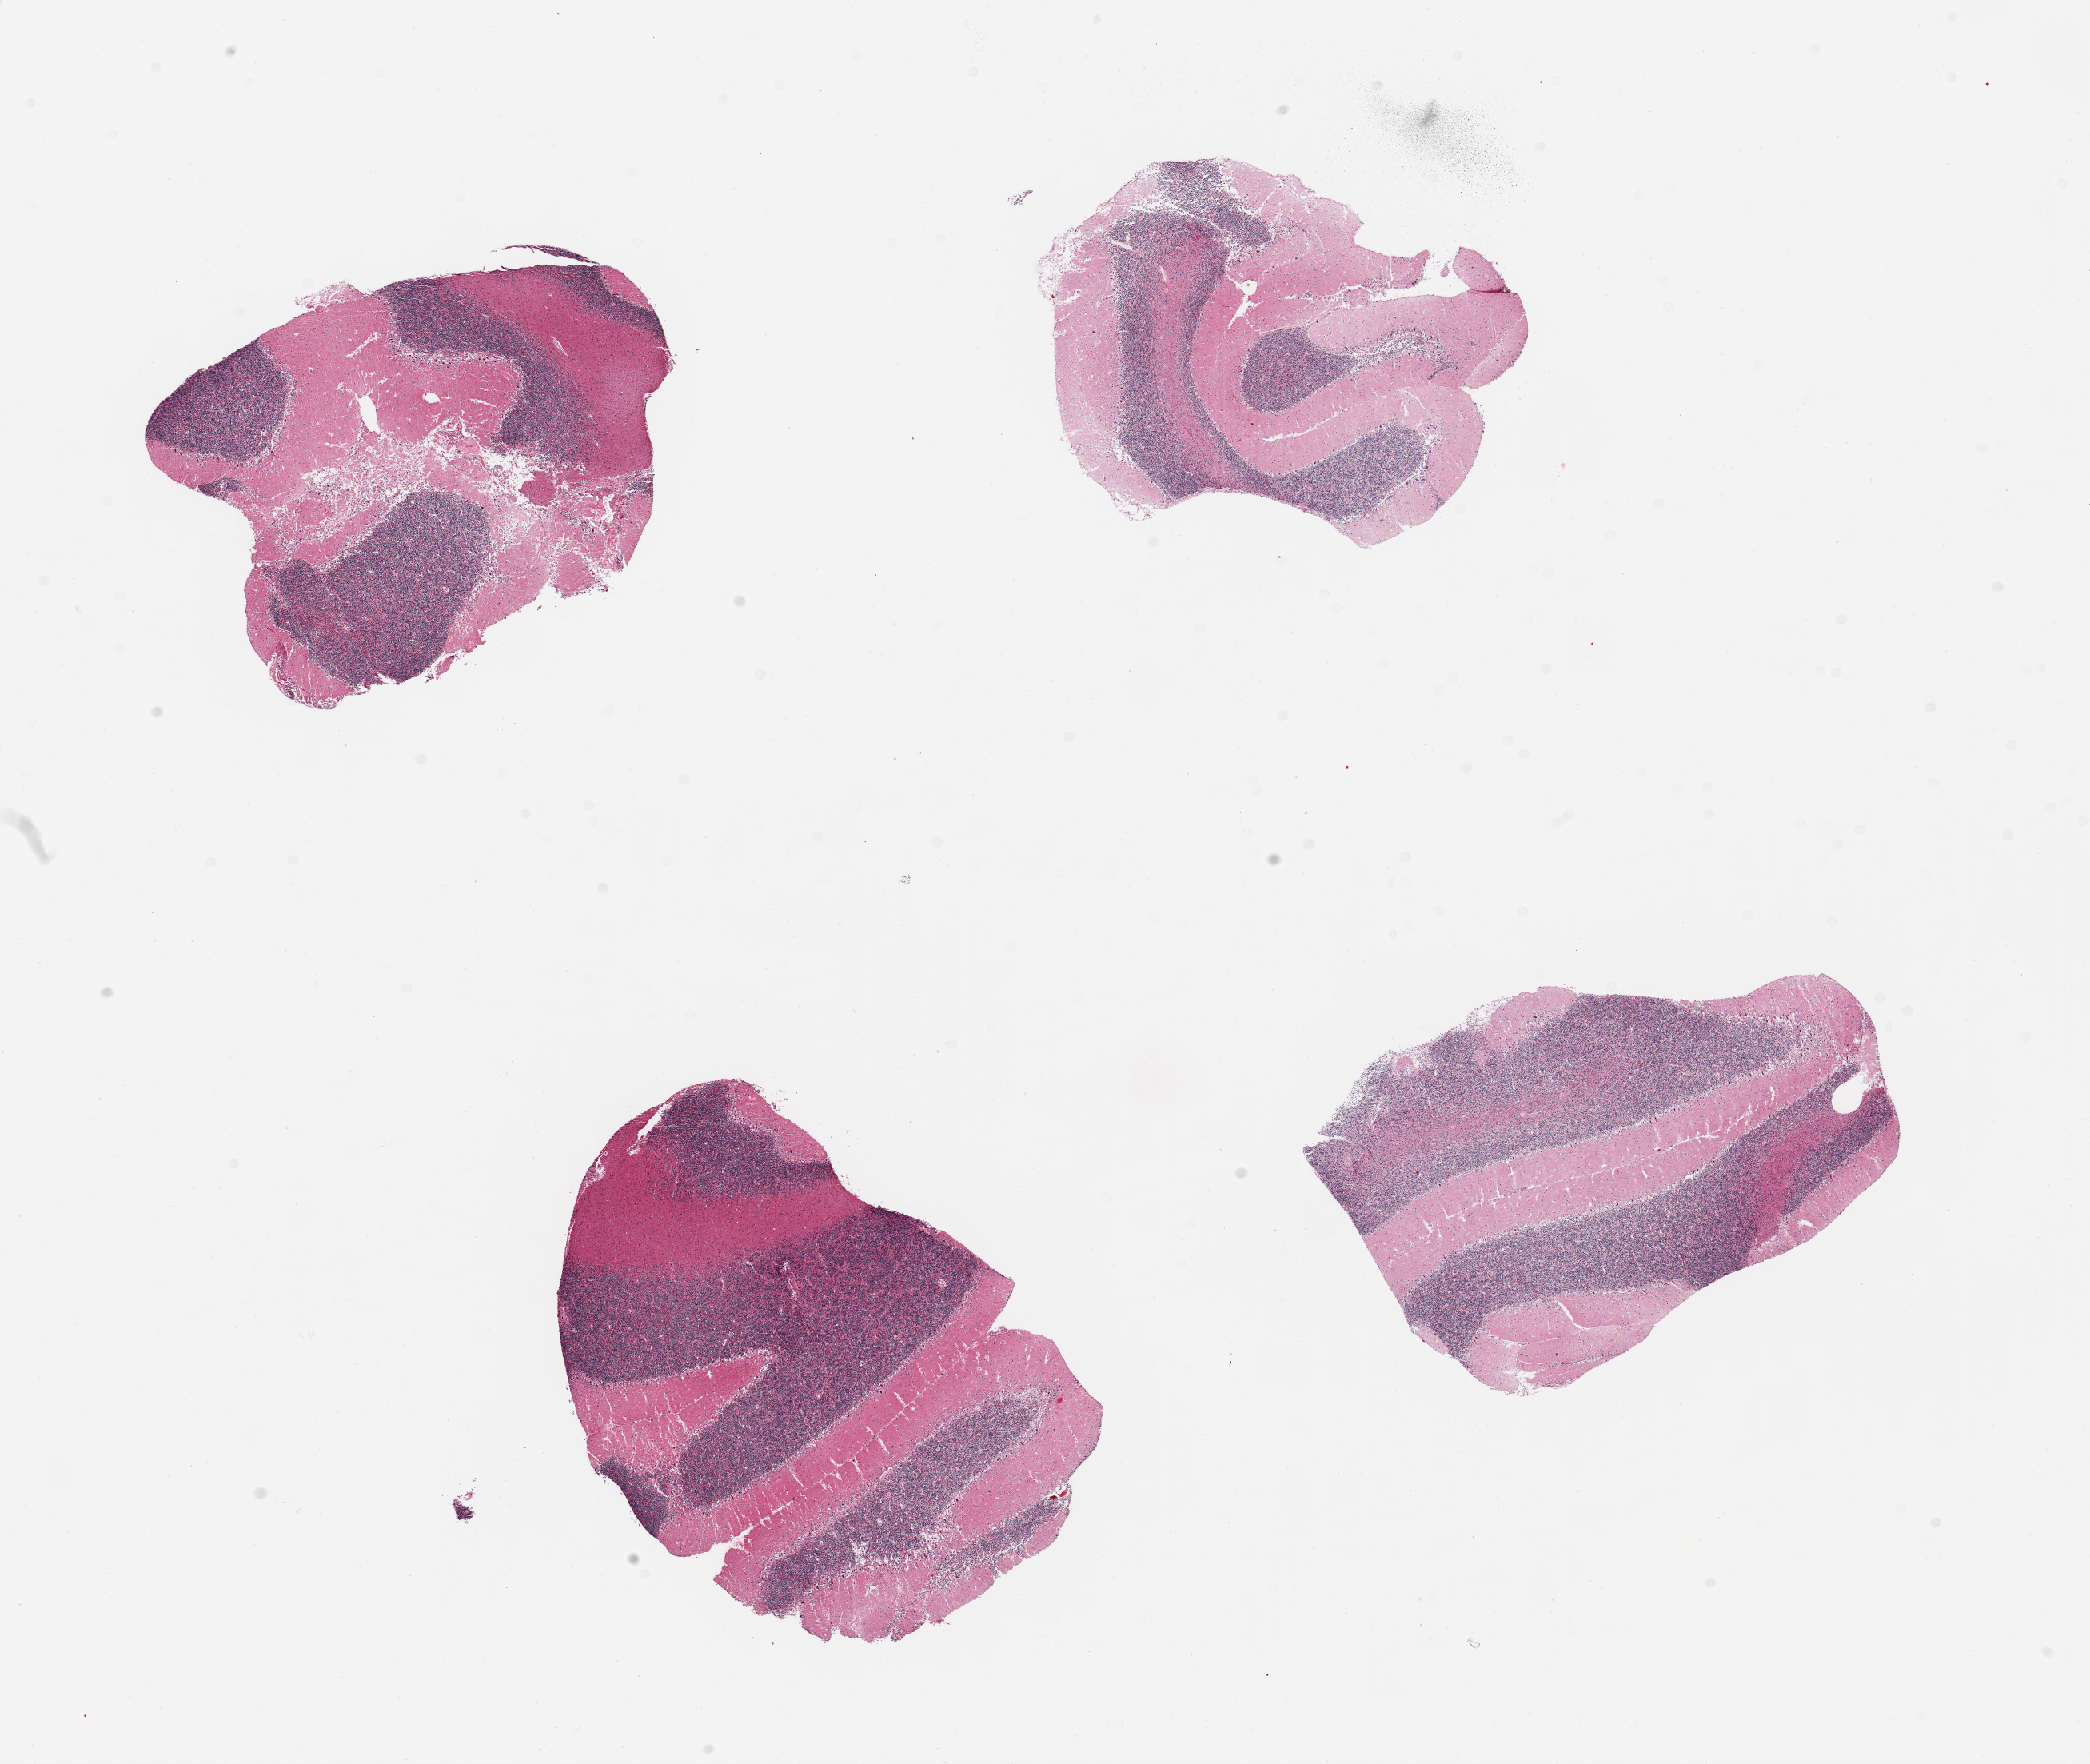
Whole-slide image, hematoxylin and eosin (H&E) stain — a low-resolution overview of the entire scanned area, about 20.7 x 17.4 mm; PAXgene-fixed, paraffin-embedded tissue; section of cerebellum (target tissue); tissue donor sample. Donor sex: male.
- pathologist's review note for this sample: 4 pieces, no abnormalities; Purkinje cells well visualized